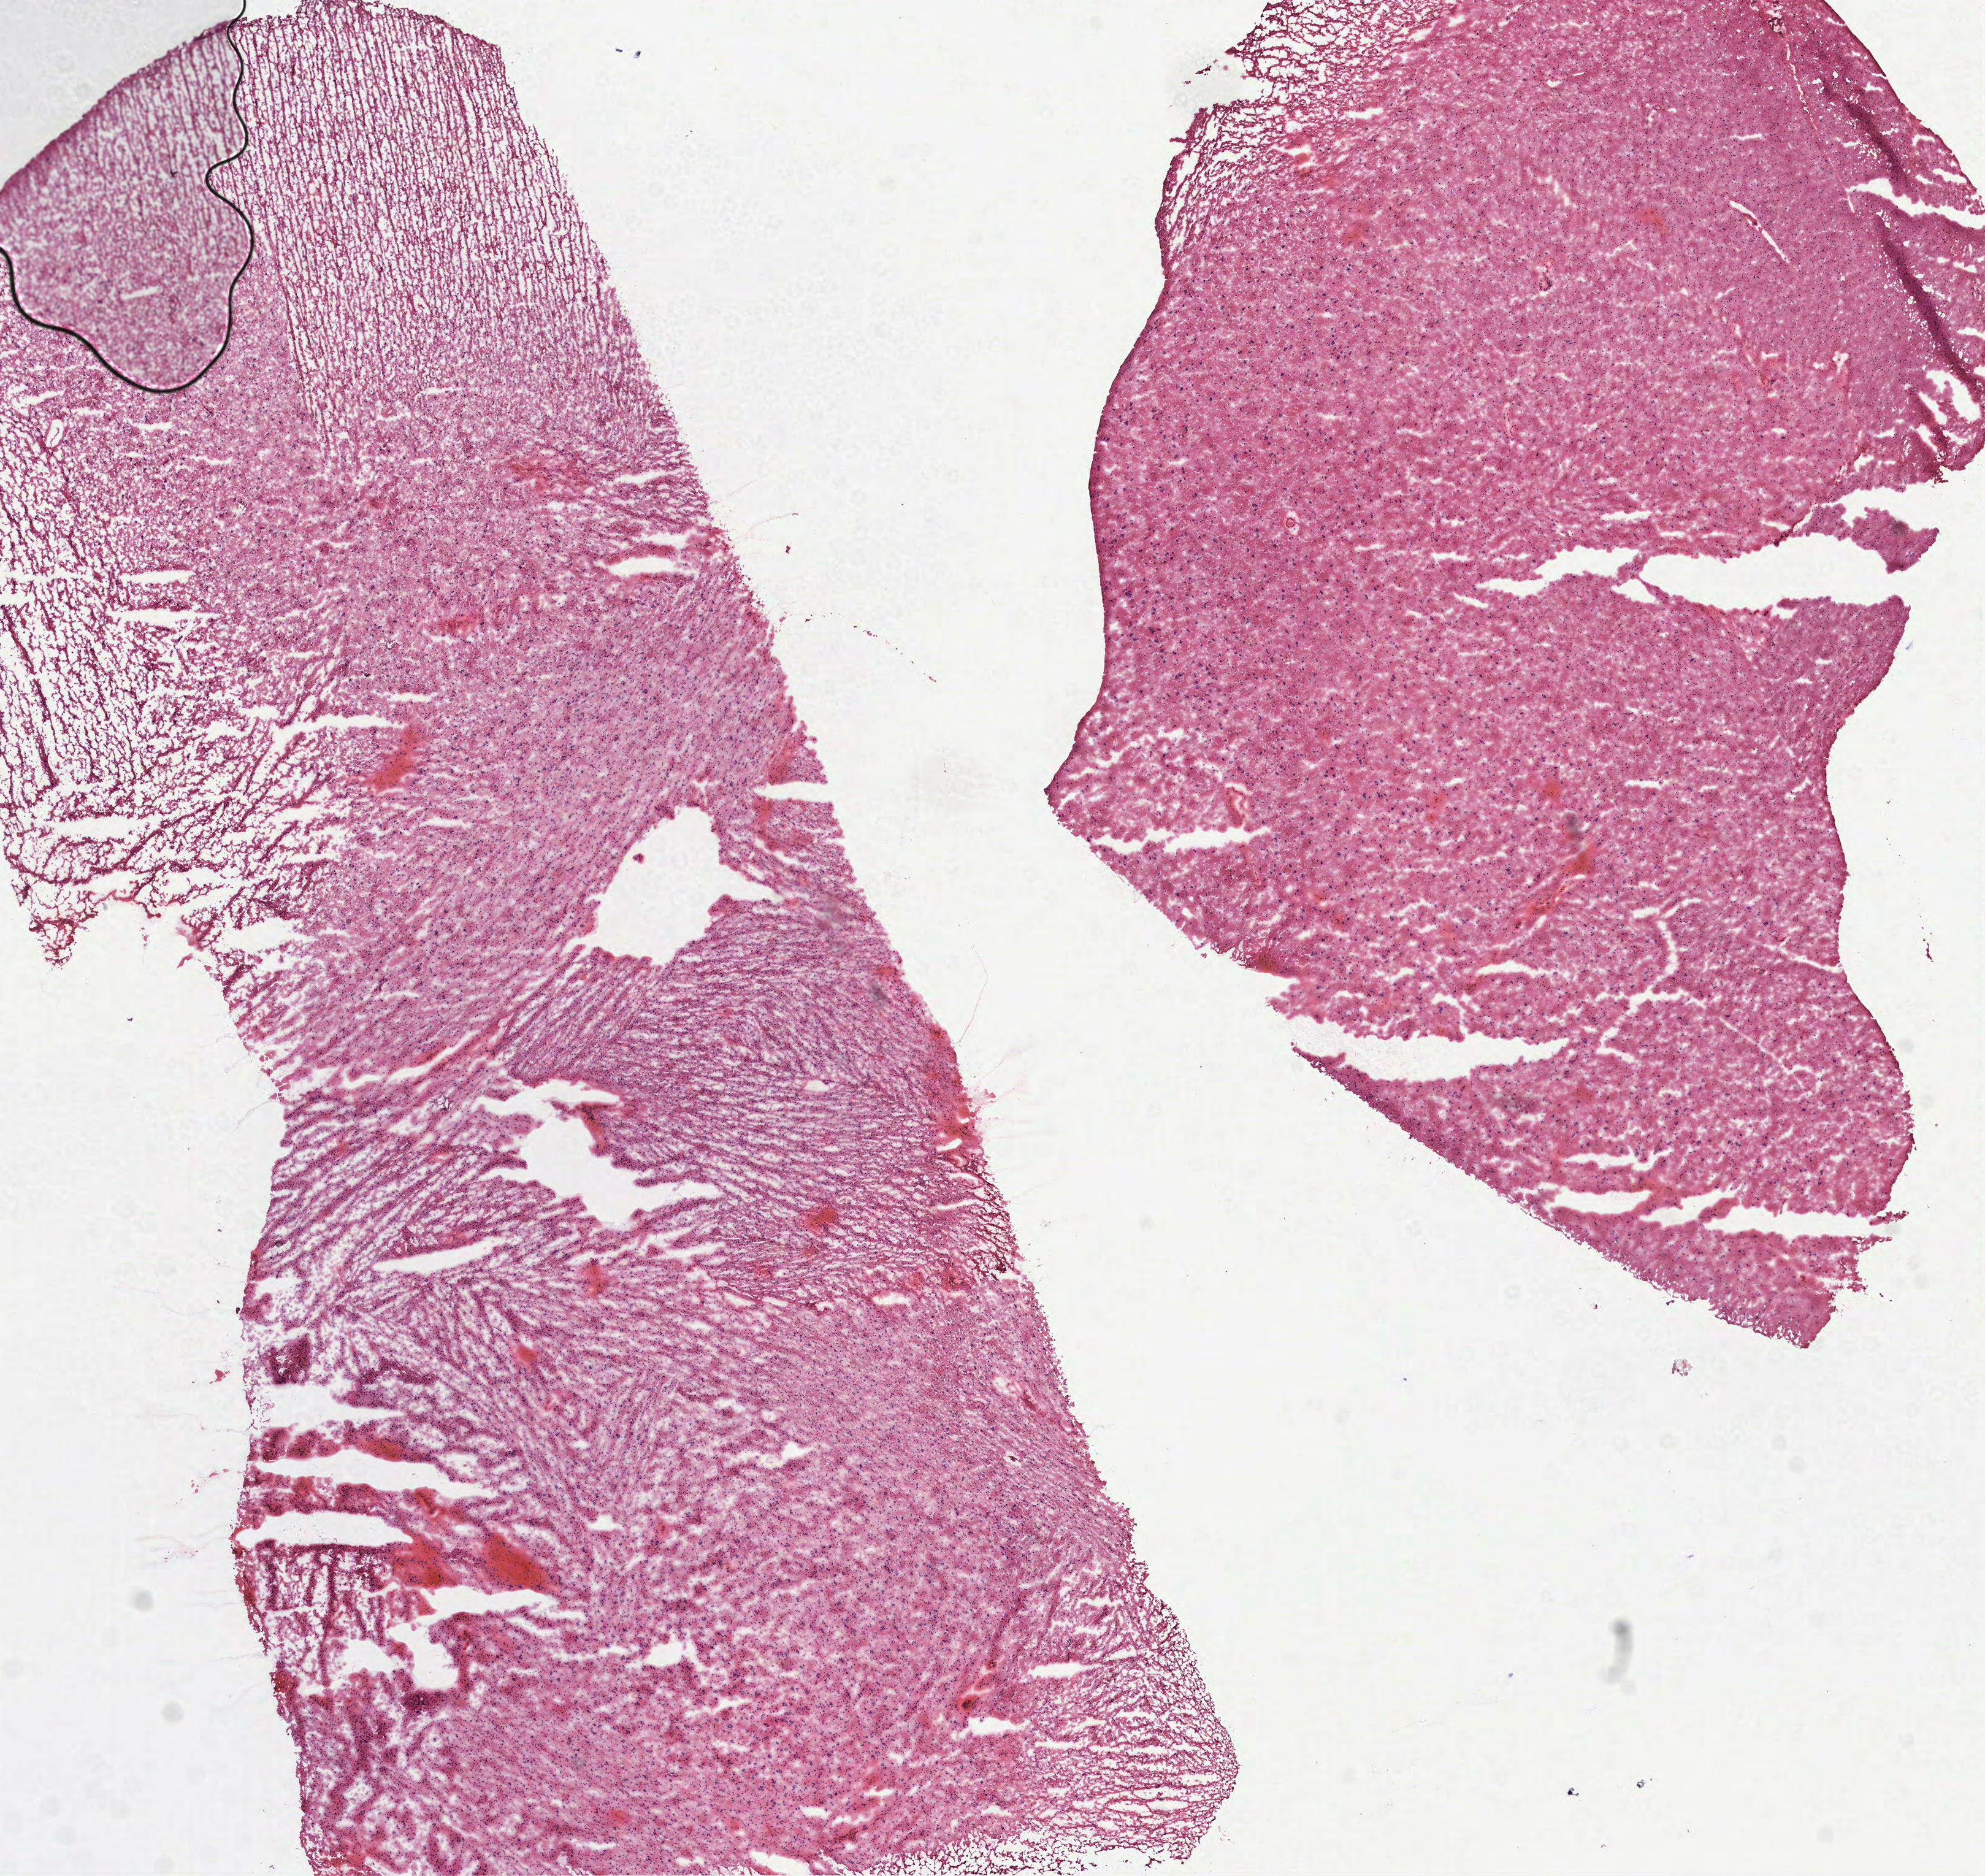
Digitized H&E-stained tissue section (whole slide) — a low-resolution overview of the entire scanned area, about 13.1 x 12.3 mm (from a 40x scan); frozen section from the top of the tissue portion; brain, primary tumour sample. Female patient; age at initial diagnosis 26 years.
Diagnosis: Oligodendroglioma, NOS.